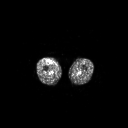
FDG PET of an extremity soft-tissue mass (from a PET/CT study), one axial slice; position 223 of 311 along the scan axis; 3.27 mm slice thickness; 128 × 128 image matrix, field of view 700 × 700 mm. Male patient, age 56 years. From the clinical record (not read from this slice): histological type: pleiomorphic leiomyosarcoma; grade: intermediate; site of the primary tumour: right thigh.
Structures marked on this image (expert contour drawn on MRI and transferred to this co-registered scan by the dataset authors):
- gross tumour volume including surrounding oedema: bounding box (x1, y1, x2, y2) in pixels: (47, 60, 50, 62)